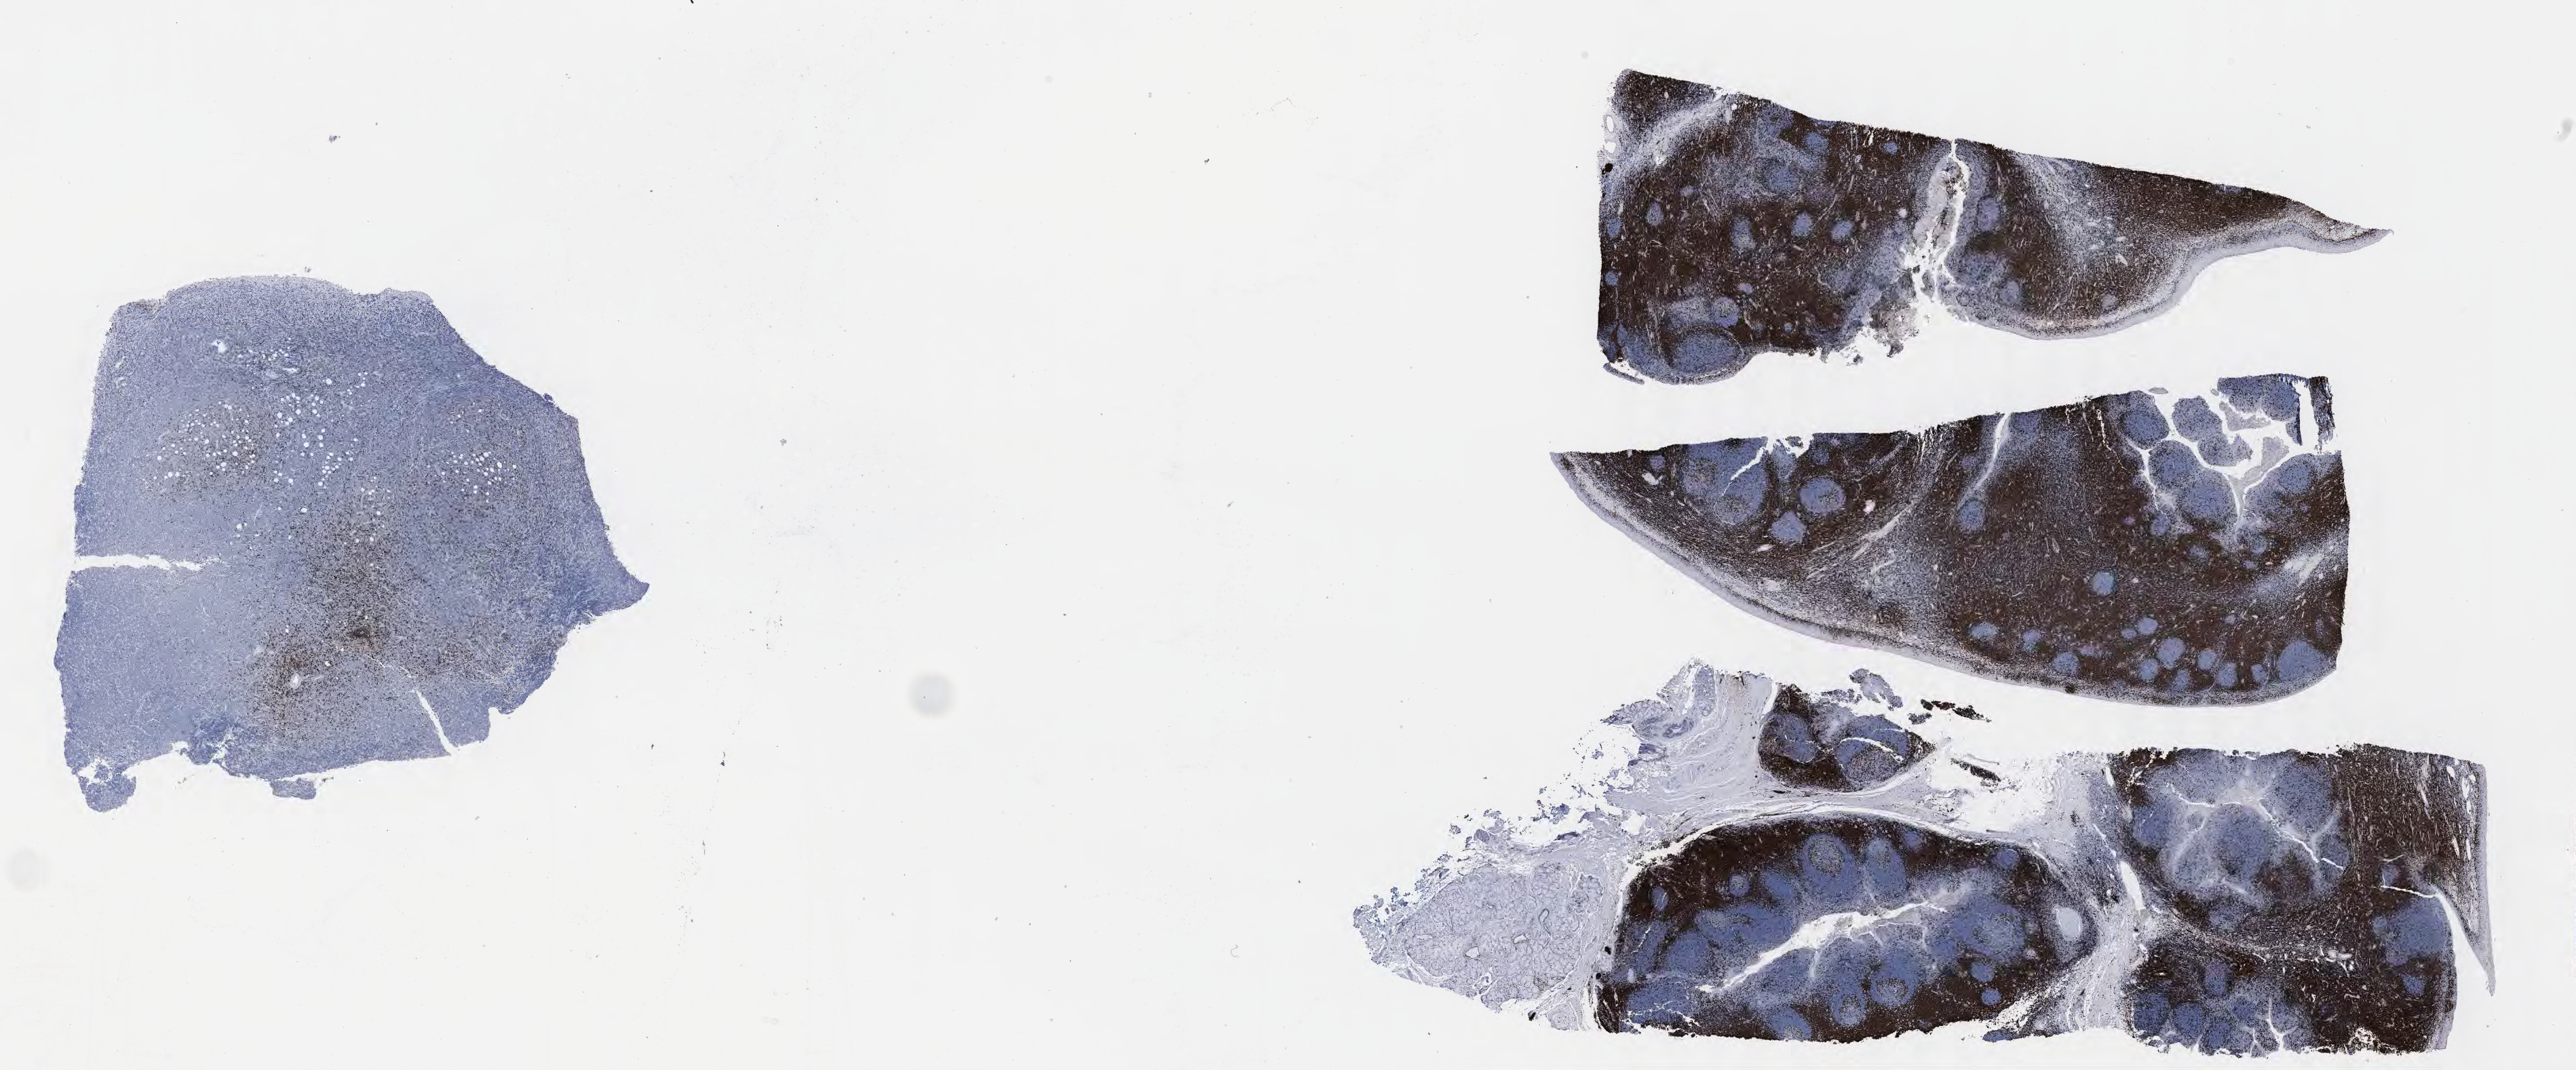
IHC for CD3, whole-slide image, whole scanned area (about 30.7 x 12.7 mm) shown as a low-resolution overview; tumor tissue; site: retroperitoneum. Male patient; age at initial diagnosis 7 years.
- diagnosis: Diffuse large B-cell lymphoma, NOS